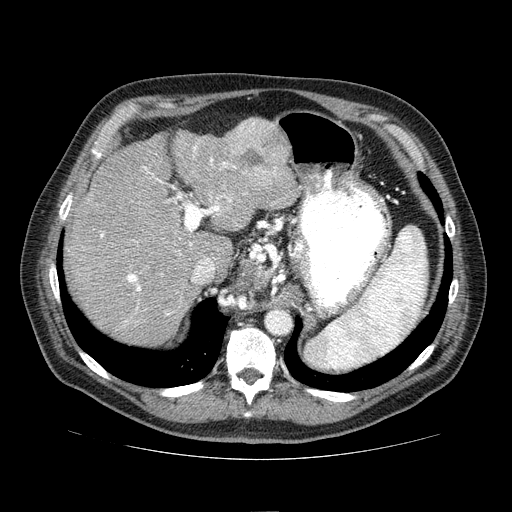
Contrast-enhanced abdominal CT (liver protocol), one axial slice; position 53 of 81 along the scan axis; 100 kVp; one of 2 acquisitions stored at this slice position; soft-tissue window (W 400 / L 40 HU); 2.5 mm slice thickness; 512 × 512 image matrix. From the clinical record (not read from this slice): diagnosis: hepatocellular carcinoma (patient treated with transarterial chemoembolisation; whether this scan precedes or follows treatment is not stated here); TNM stage (as recorded): Stage-IIIA; Child-Pugh class: A; tumour nodularity: multinodular.
Structures marked on this image (semi-automatically segmented with operator editing):
- liver parenchyma outside the tumour (the mass and vessels are separate outlines, so this box may not span the whole liver): box from (x=66, y=118) to (x=296, y=344) px
- mass: (x=220, y=118)–(x=289, y=187)
- liver vessels: (x=100, y=145)–(x=247, y=323)